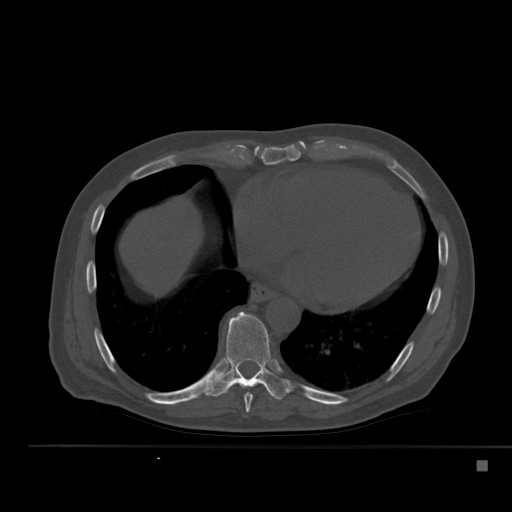
CT including the spine, one axial slice. Slice 293 of 517 in the series (ordered by position). Reconstruction kernel Br40s. 120 kVp. Bone window (W 1800 / L 400 HU). 512 × 512 image matrix. Patient: male, 70 years. Case-level facts recorded for this patient, not image findings: primary cancer: renal; vertebrae with lytic lesions (as recorded): T4, T6, T10, T12, L3, L4, L5.
Structures marked on this image (semi-automatically segmented with operator editing):
- T8 vertebra: bounding box (x1, y1, x2, y2) in pixels: (244, 383, 259, 412)
- T9 vertebra: (207, 311, 289, 400)